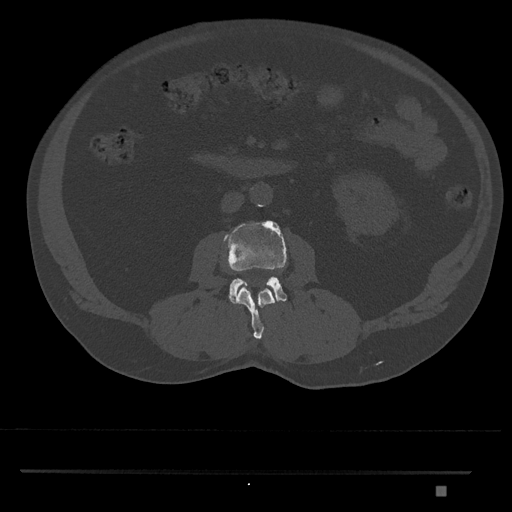
CT including the spine, one axial slice. Position 715 of 1134 along the scan axis. Reconstruction kernel Br40s/3. Bone window (W 1800 / L 400 HU). 512 × 512 image matrix, field of view 429 × 429 mm. Male patient, age 65 years. From the clinical record (not read from this slice): primary cancer: prostate.
Outlined on this slice (semi-automatically segmented with operator editing):
- L2 vertebra: bounding box (x1, y1, x2, y2) in pixels: (237, 286, 275, 339)
- L3 vertebra: (223, 220, 287, 305)